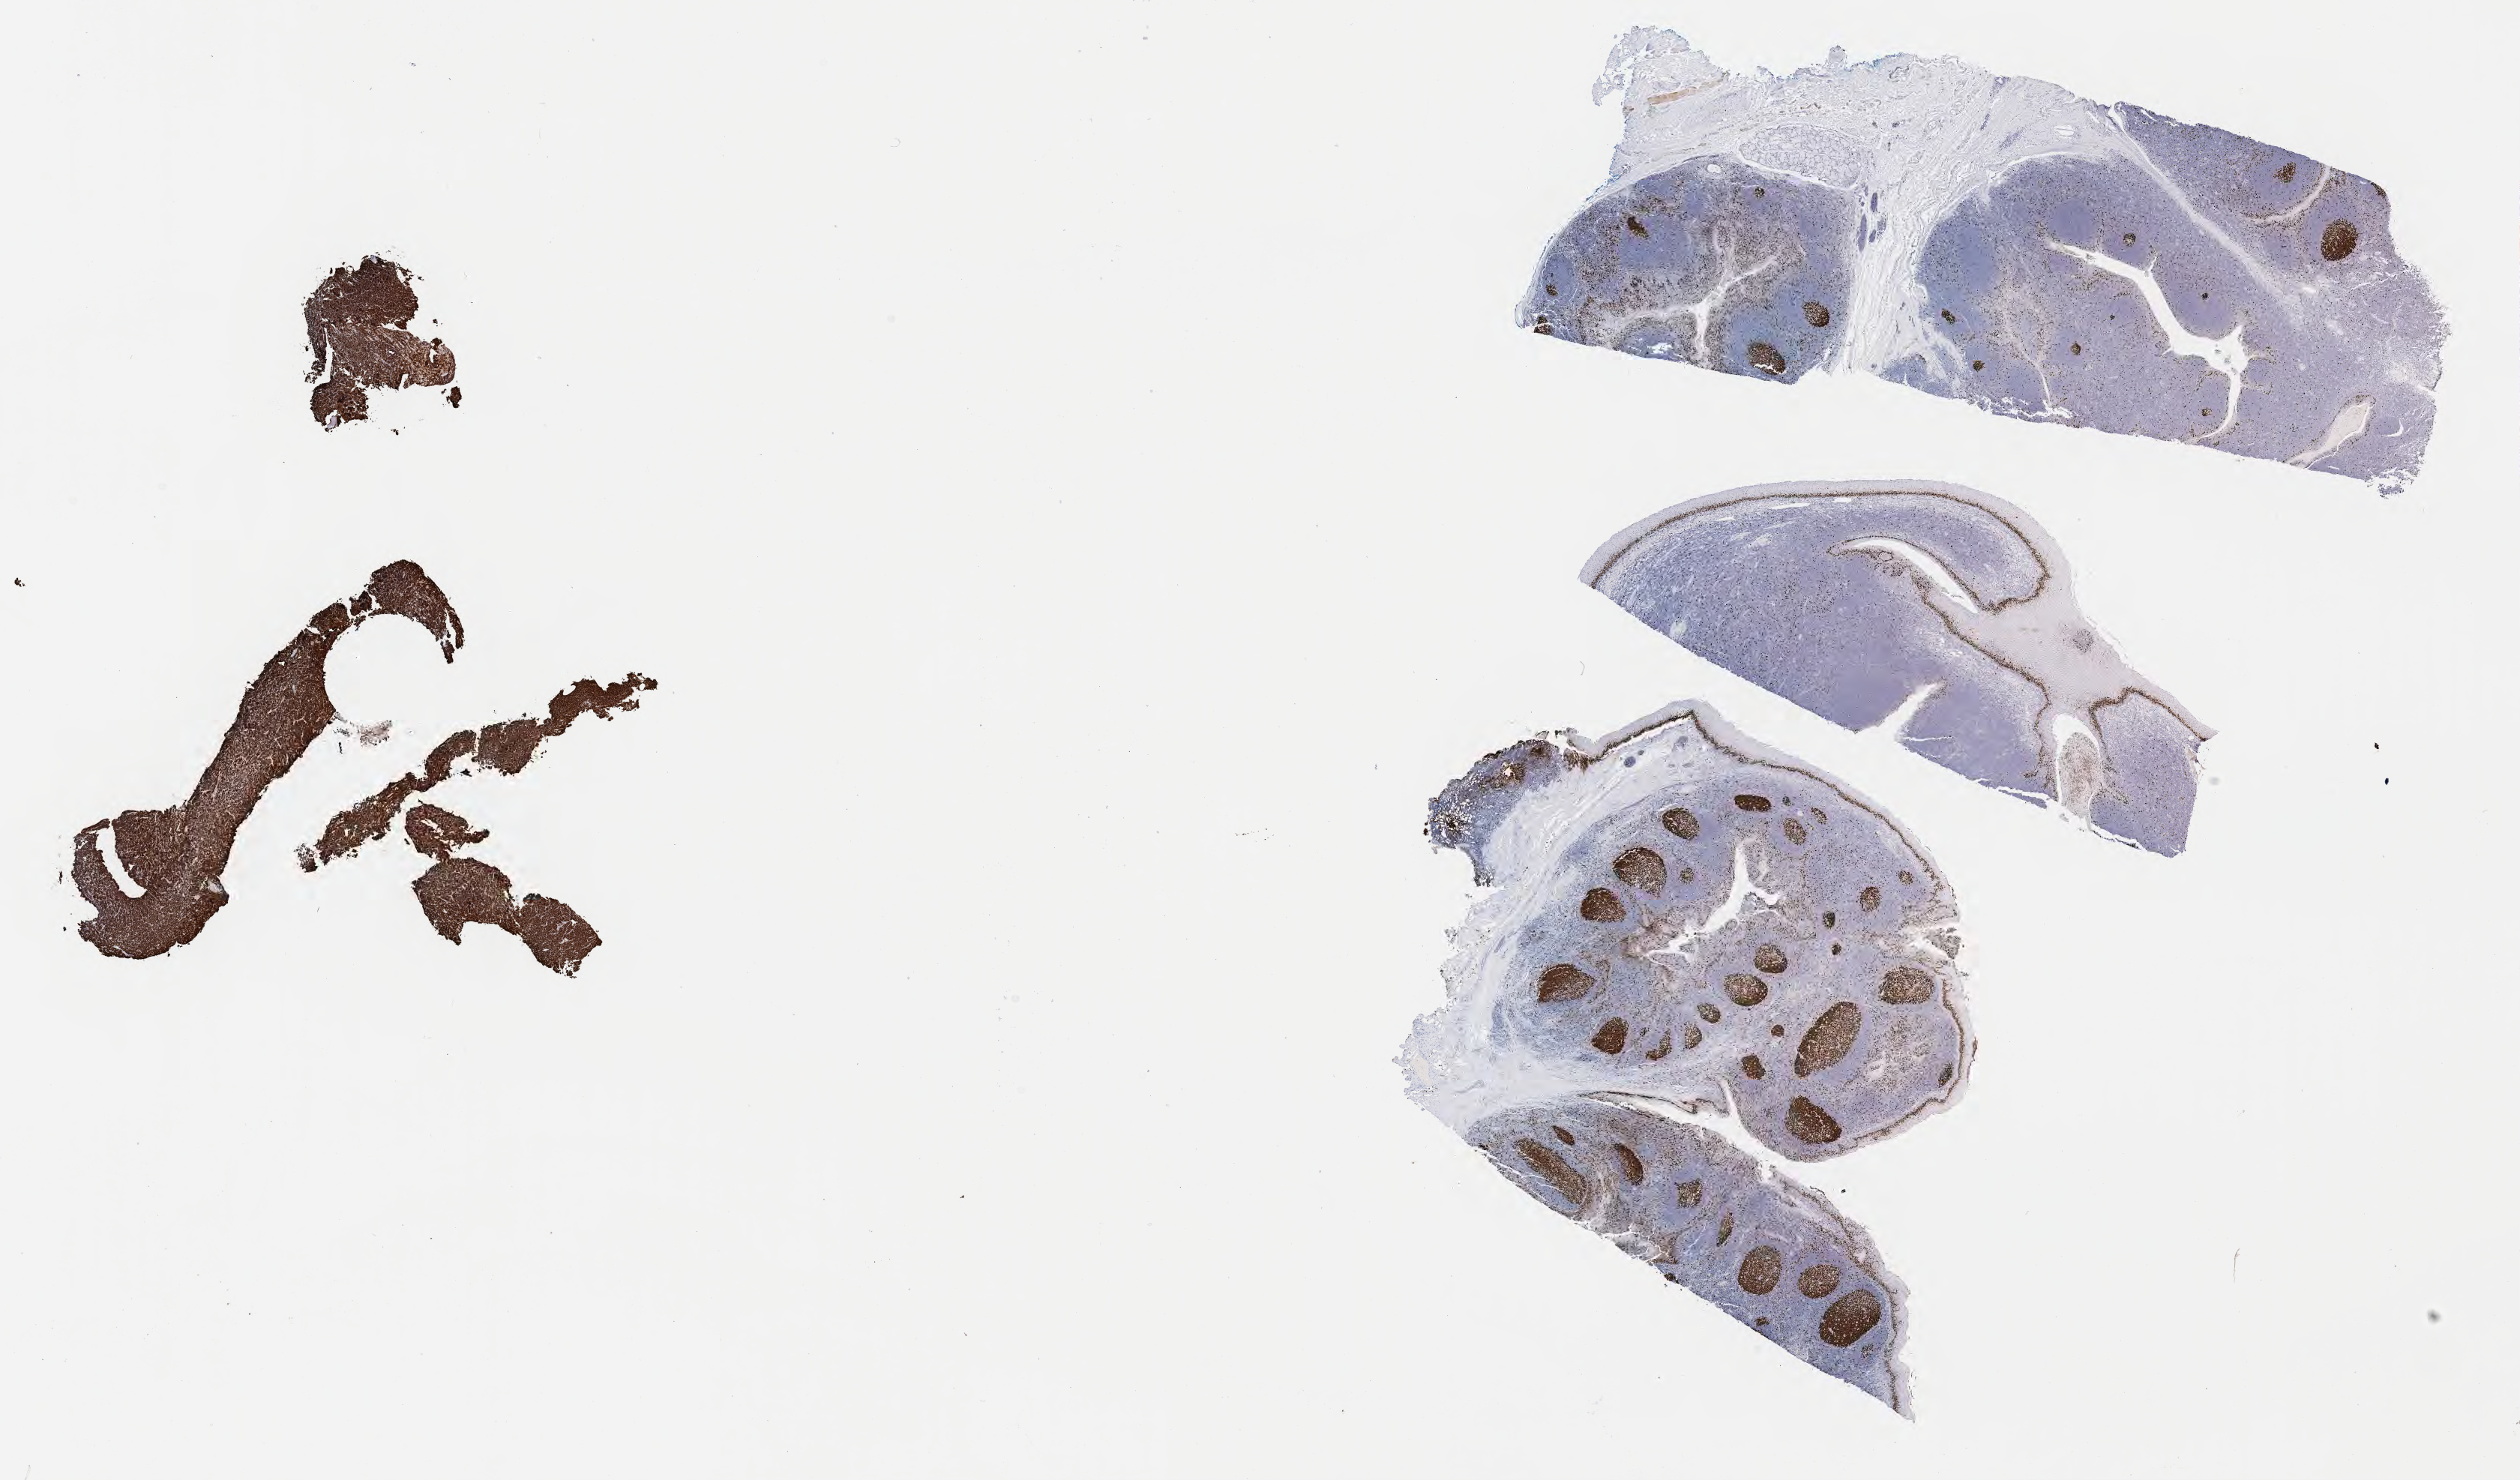
Immunohistochemistry (IHC) whole-slide image stained for Ki-67, low-resolution overview of the scanned area, about 27.2 x 16.0 mm. Specimen: tumor tissue. Anatomic site: cranium. Male, age 5 years at initial diagnosis.
Diagnosis: Burkitt lymphoma, NOS.